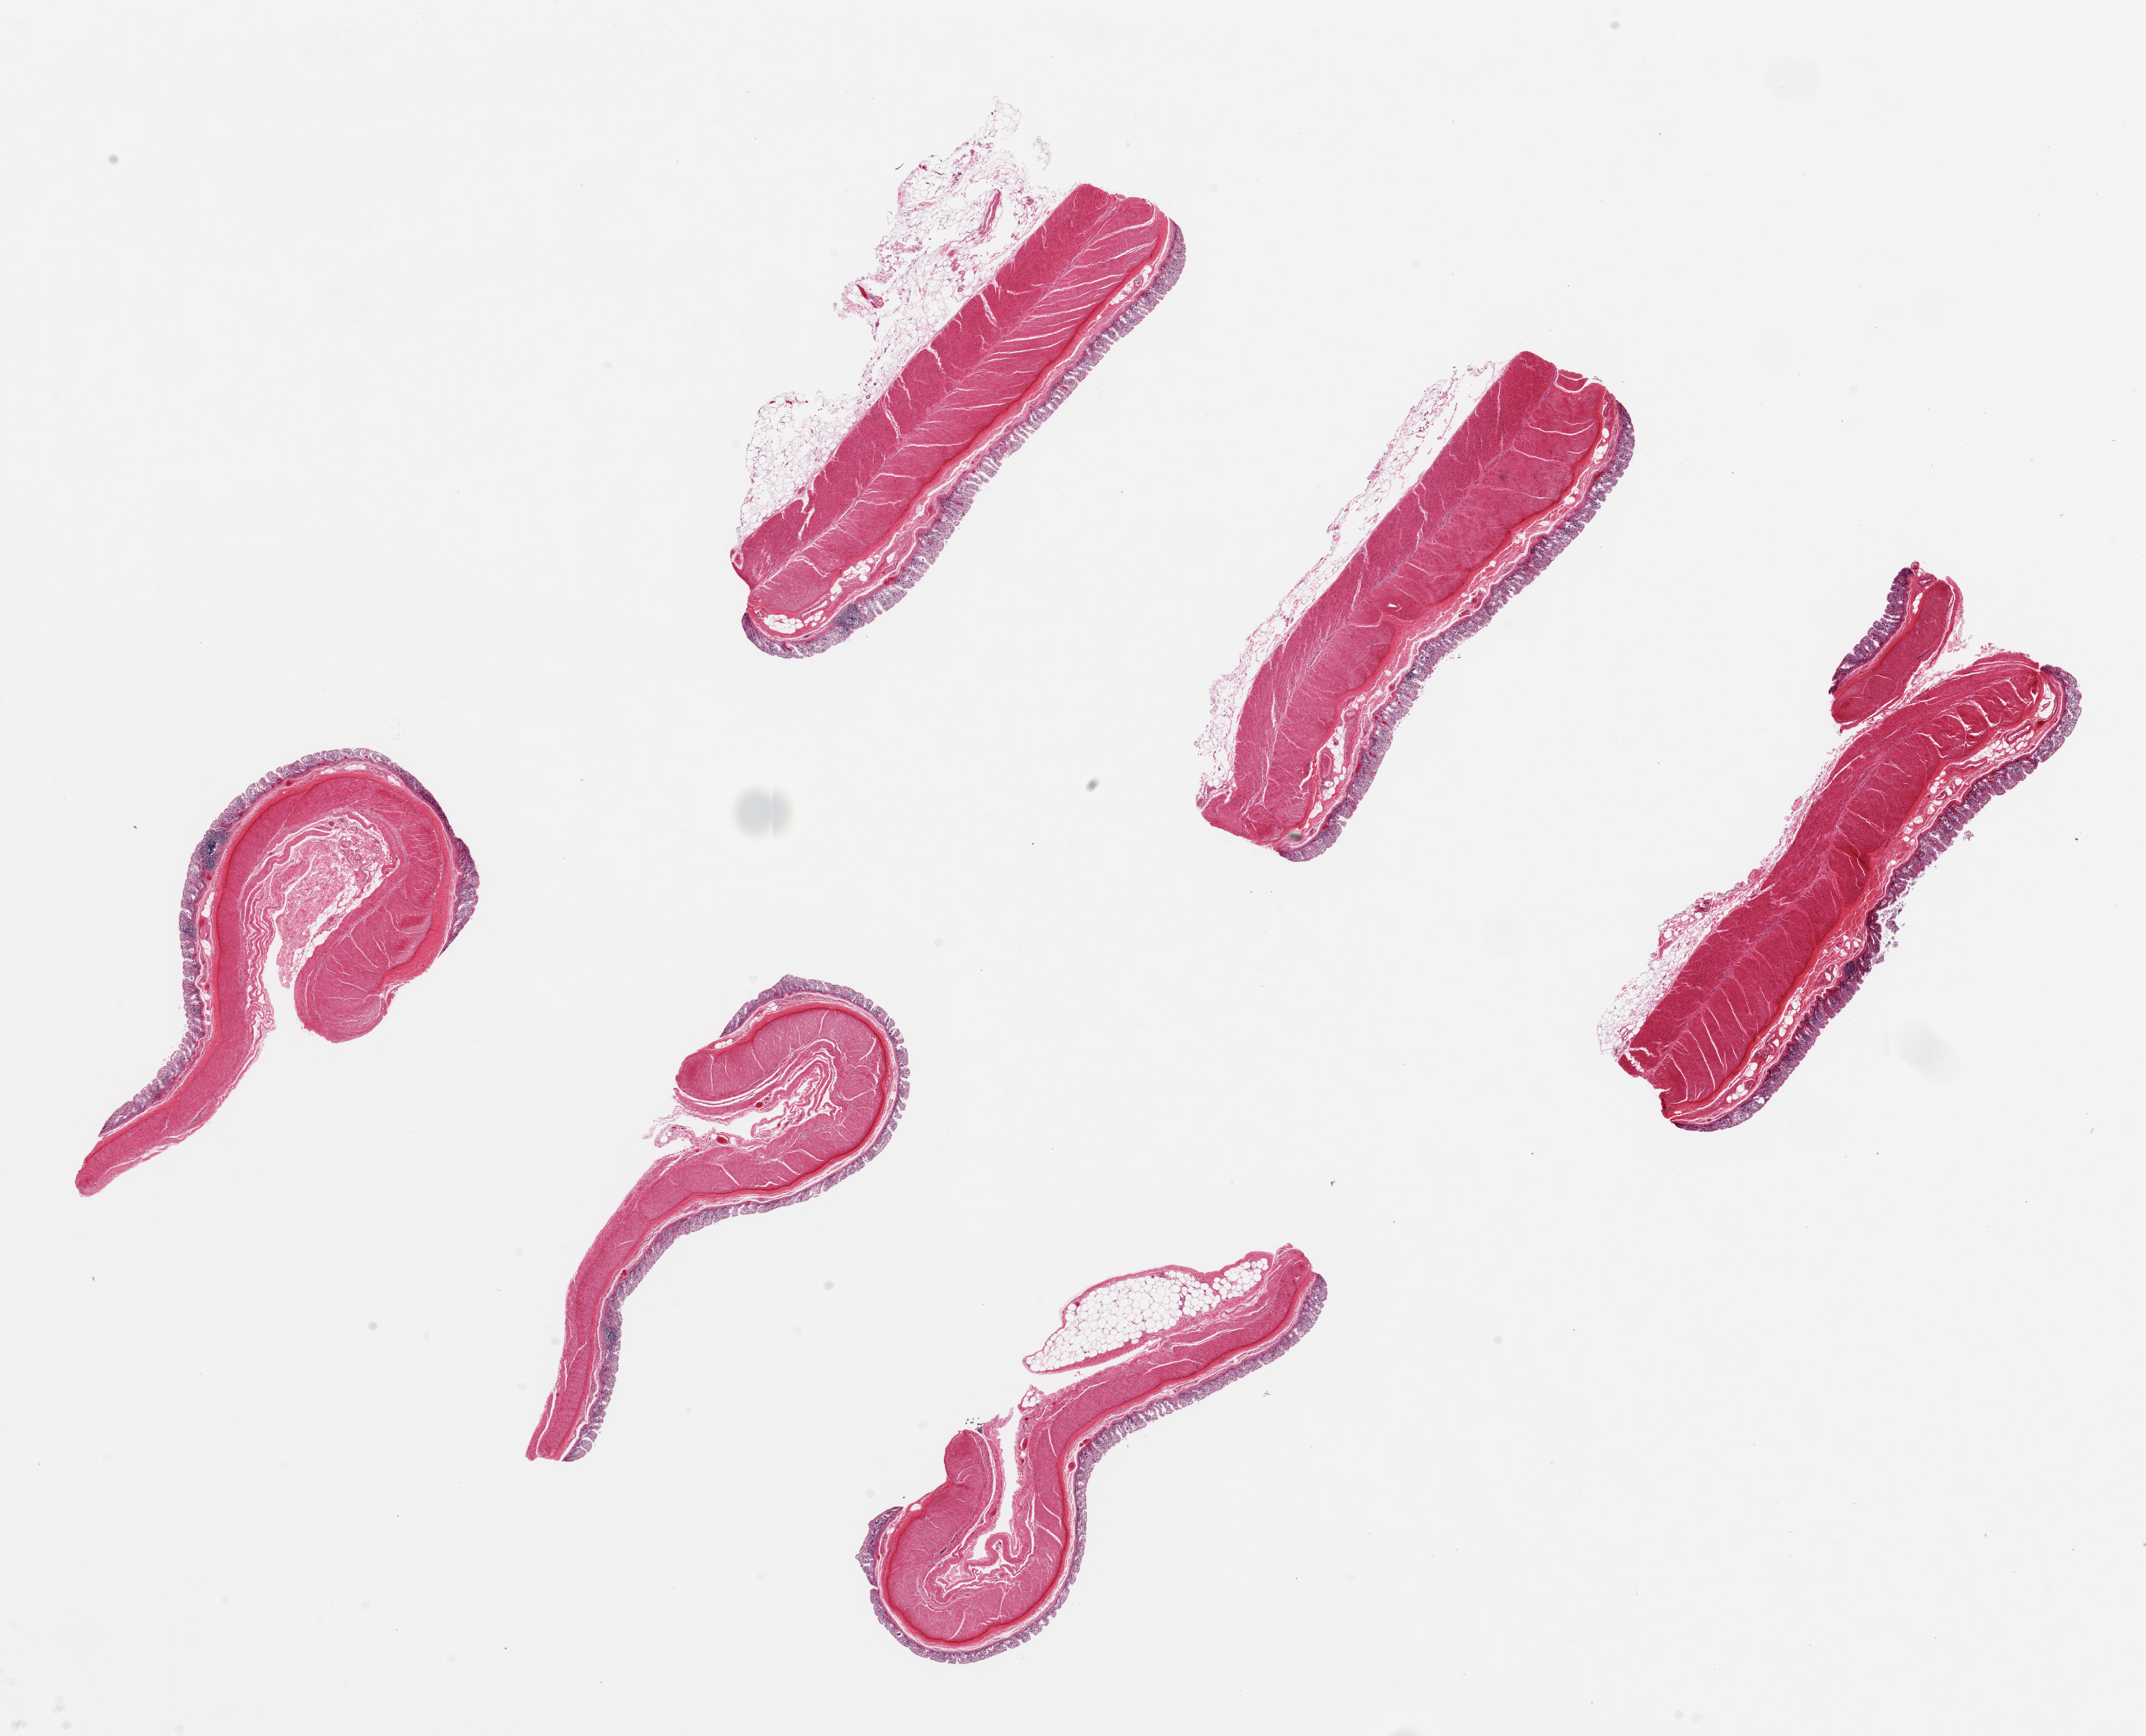
Whole-slide image, haematoxylin and eosin stain, a low-resolution overview of the entire scanned area, about 24.6 x 19.9 mm. PAXgene-fixed, paraffin-embedded tissue. Target tissue: transverse colon. Tissue donor sample. Male donor.
Pathologist's review note for this sample: 6 pieces, ~6.5x1.5mm. Mucosa severely autolyzed.